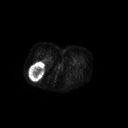
FDG PET of an extremity soft-tissue mass (from a PET/CT study), one axial slice. 3.27 mm slice thickness. 128 × 128 image matrix. Female patient, age 70 years. From the clinical record (not read from this slice): histological type: synovial sarcoma; grade: intermediate; site of the primary tumour: right buttock.
Annotated regions visible in this slice (expert contour drawn on MRI and transferred to this co-registered scan by the dataset authors):
- gross tumour volume including surrounding oedema: bounding box (x1, y1, x2, y2) in pixels: (29, 62, 45, 80)
- gross tumour volume (mass): (29, 62, 45, 80)